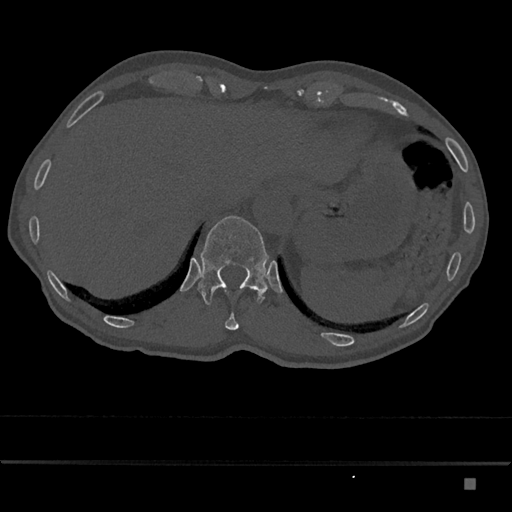
CT including the spine, one axial slice. Slice 632 of 797 in the series (ordered by position). Reconstruction kernel Br40s/3. Bone window (W 1800 / L 400 HU). 0.5 mm slice thickness. 512 × 512 image matrix, field of view 390 × 390 mm. Patient: male, 72 years. Case-level facts recorded for this patient, not image findings: primary cancer: prostate.
Outlined on this slice (semi-automatic segmentation, software-assisted and operator-edited):
- T11 vertebra: bounding box <225,312,239,330> (left, top, right, bottom; pixels)
- T12 vertebra: <197,216,269,305>